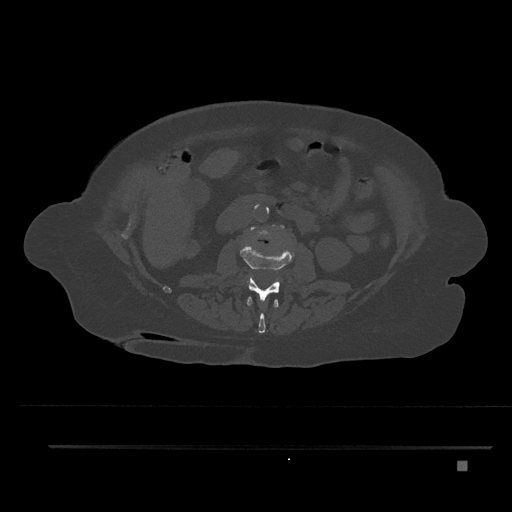
CT including the spine, one axial slice. Position 171 of 797 along the scan axis. Reconstruction kernel Br40s/3. Bone window (W 1800 / L 400 HU). 0.5 mm slice thickness. 512 × 512 image matrix, field of view 437 × 437 mm. Patient: female, 76 years. Case-level facts recorded for this patient, not image findings: primary cancer: lung; vertebrae with lytic lesions (as recorded): T11, L3.
Outlined on this slice (semi-automatic segmentation, software-assisted and operator-edited):
- L1 vertebra: bounding box <246,296,279,333> (left, top, right, bottom; pixels)
- L2 vertebra: <240,245,294,303>
- L3 vertebra: <248,225,284,280>